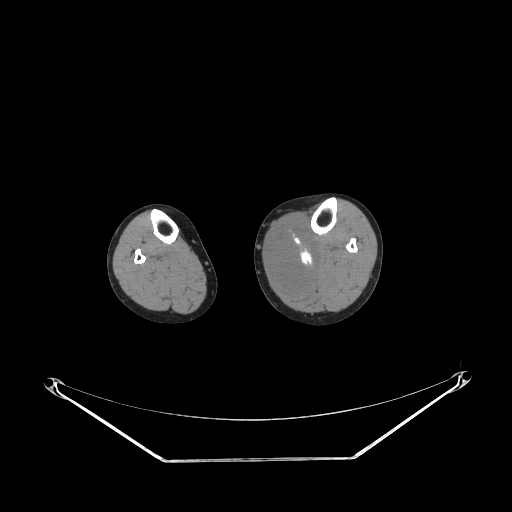
CT of an extremity soft-tissue mass (from a PET/CT study), one axial slice. Position 138 of 223 along the scan axis. Reconstruction kernel STANDARD. Soft-tissue window (W 400 / L 40 HU). 3.75 mm slice thickness. 512 × 512 image matrix. Female patient. Case-level facts recorded for this patient, not image findings: histological type: extraskeletal high grade osteogenic sarcoma; grade: high; site of the primary tumour: left calf.
Annotated regions visible in this slice (expert contour drawn on MRI and transferred to this co-registered scan by the dataset authors):
- gross tumour volume (mass): box from (x=269, y=228) to (x=316, y=287) px